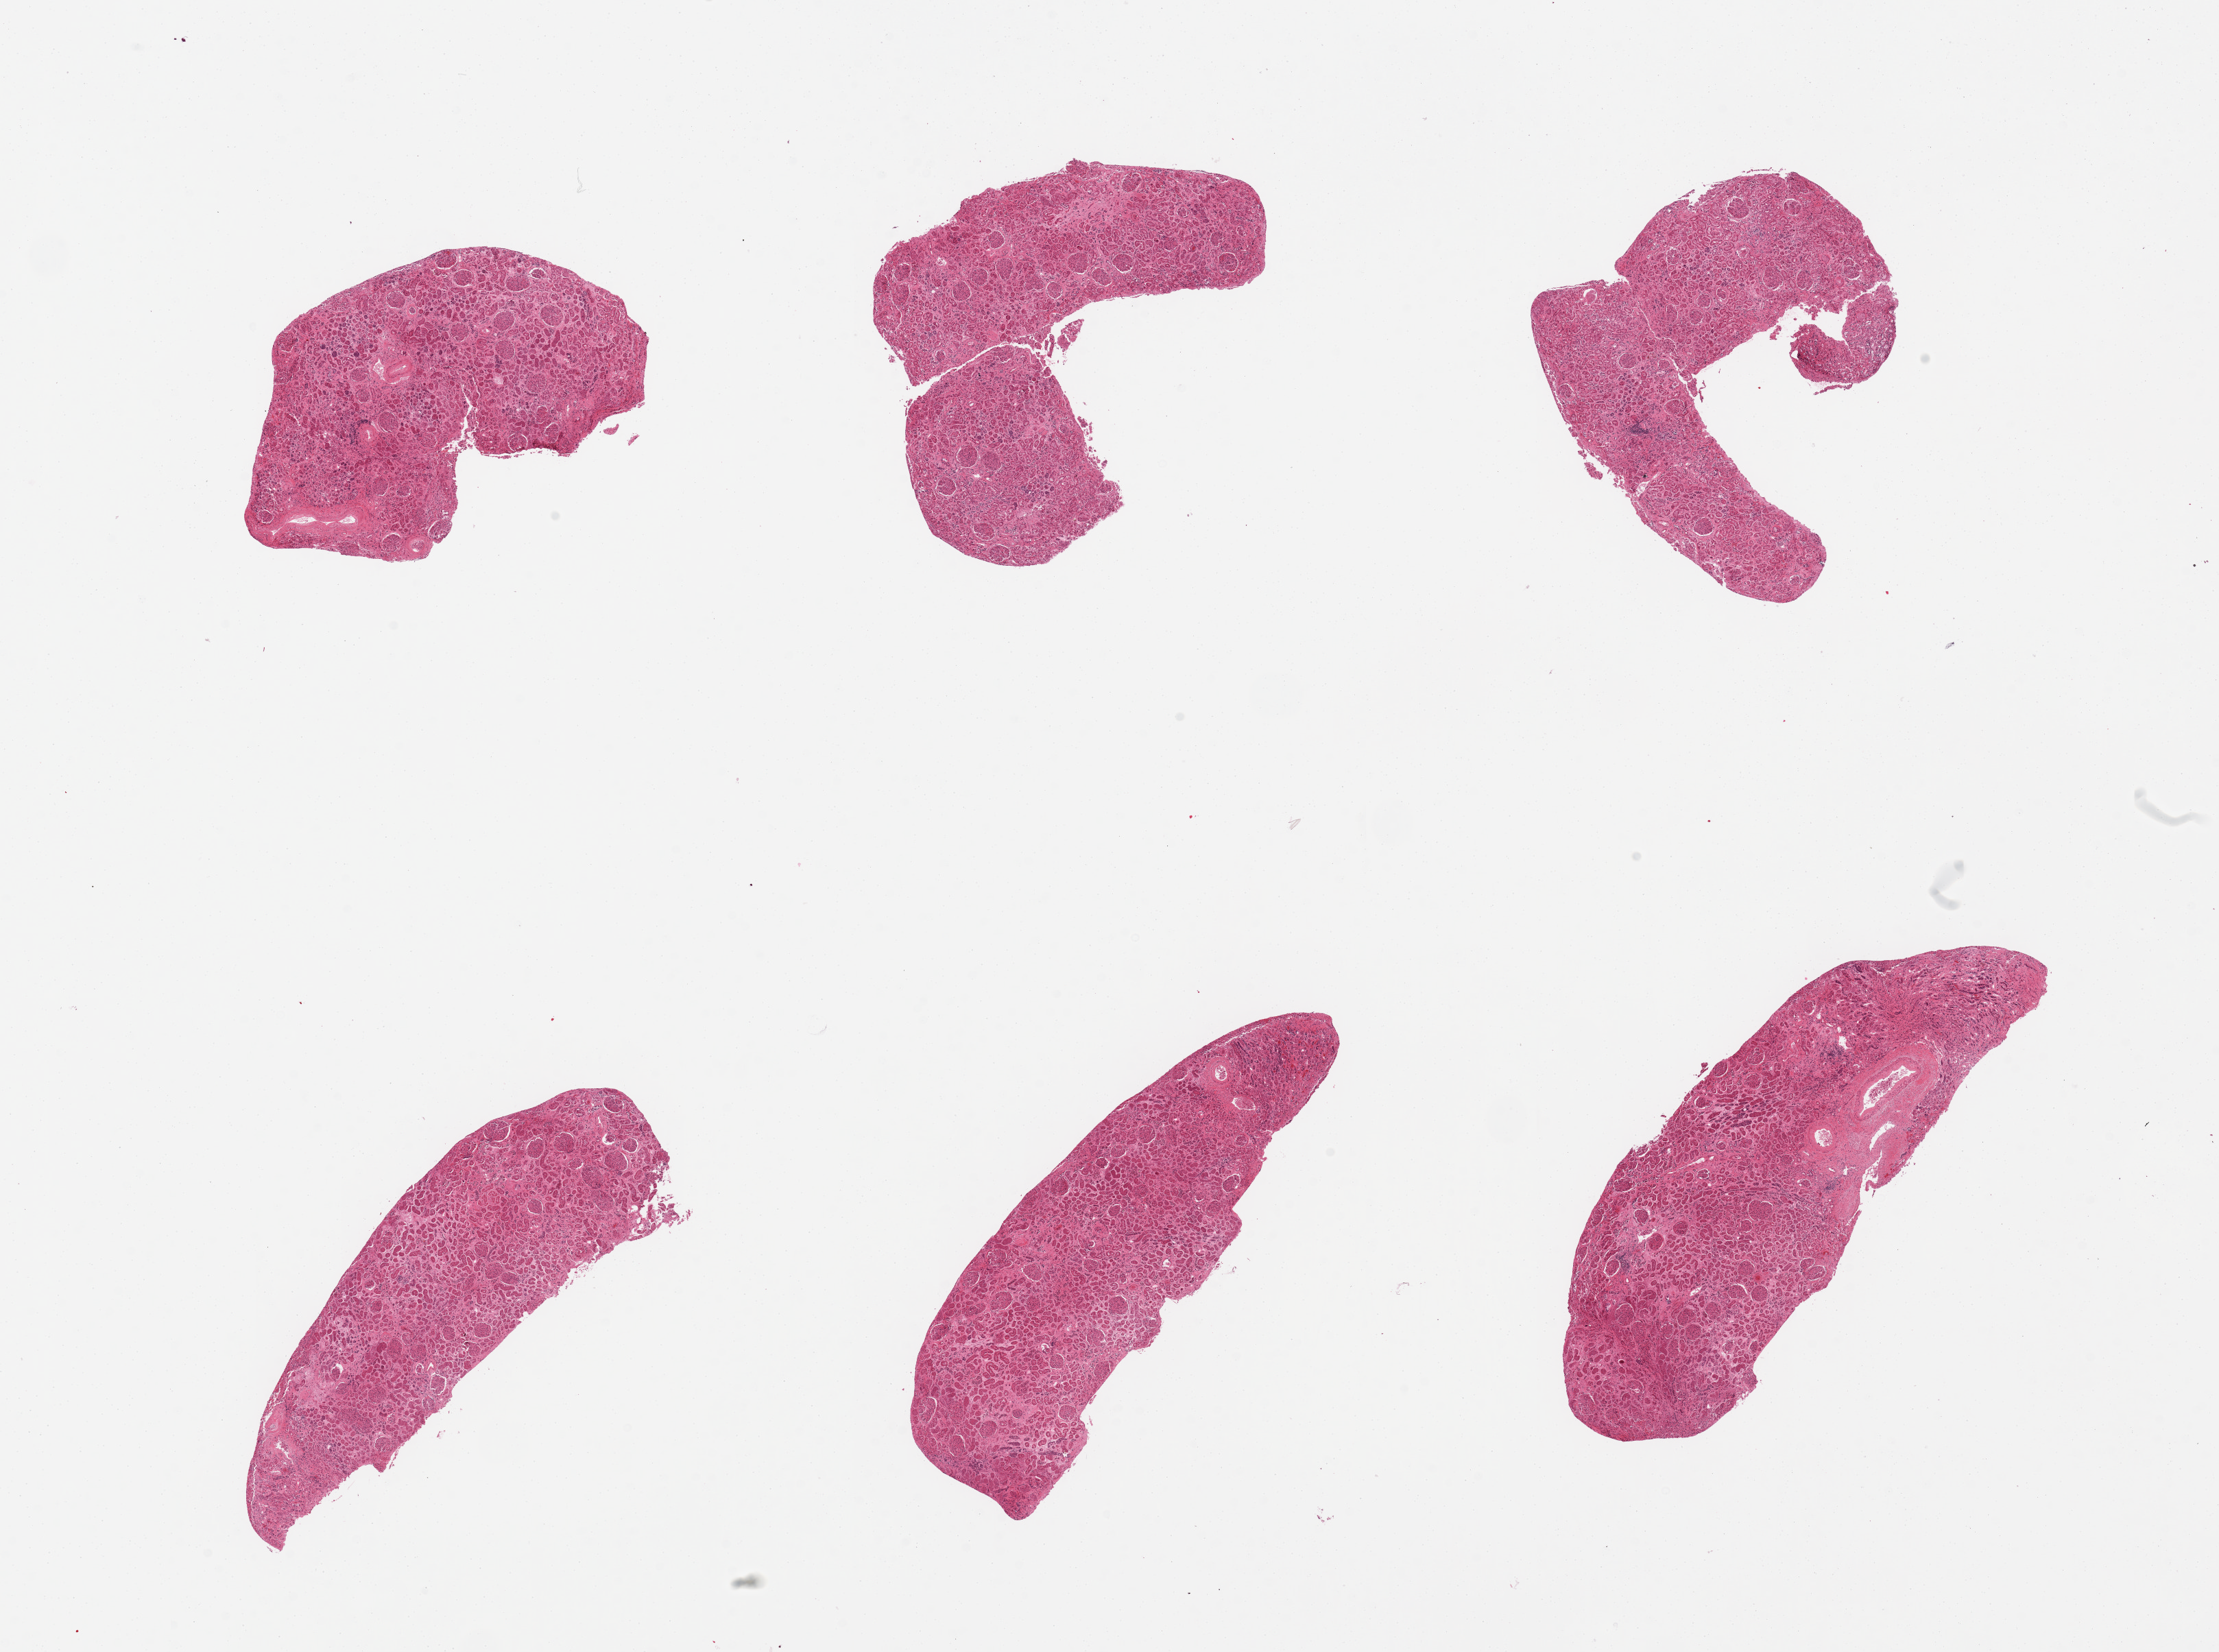
Hematoxylin and eosin (H&E) whole-slide image — low-resolution overview of the scanned area, about 25.6 x 19.1 mm. PAXgene-fixed paraffin-embedded (PFPE) section. Target tissue: renal cortex. Donor tissue sample. Donor: female.
Review note (as recorded): 6 pieces, markedly autolyzed cortex; glomeruli noted in all sections.